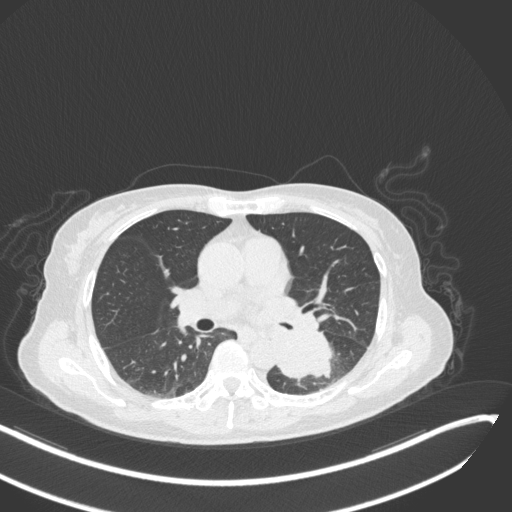
Chest CT, one axial slice; position 151 of 342 along the scan axis; reconstruction kernel B31f; 120 kVp; lung window (W 1500 / L -600 HU); 1 mm slice thickness; 512 × 512 image matrix, field of view 400 × 400 mm. Patient: female, 64 years. Case-level facts recorded for this patient, not image findings: clinical TNM (as recorded): T3 N1 M1; histopathological grade: G3.
Outlined on this slice (bounding box drawn by a radiologist):
- lung tumour (recorded histology: small cell carcinoma): bounding box (x1, y1, x2, y2) in pixels: (271, 325, 339, 388)